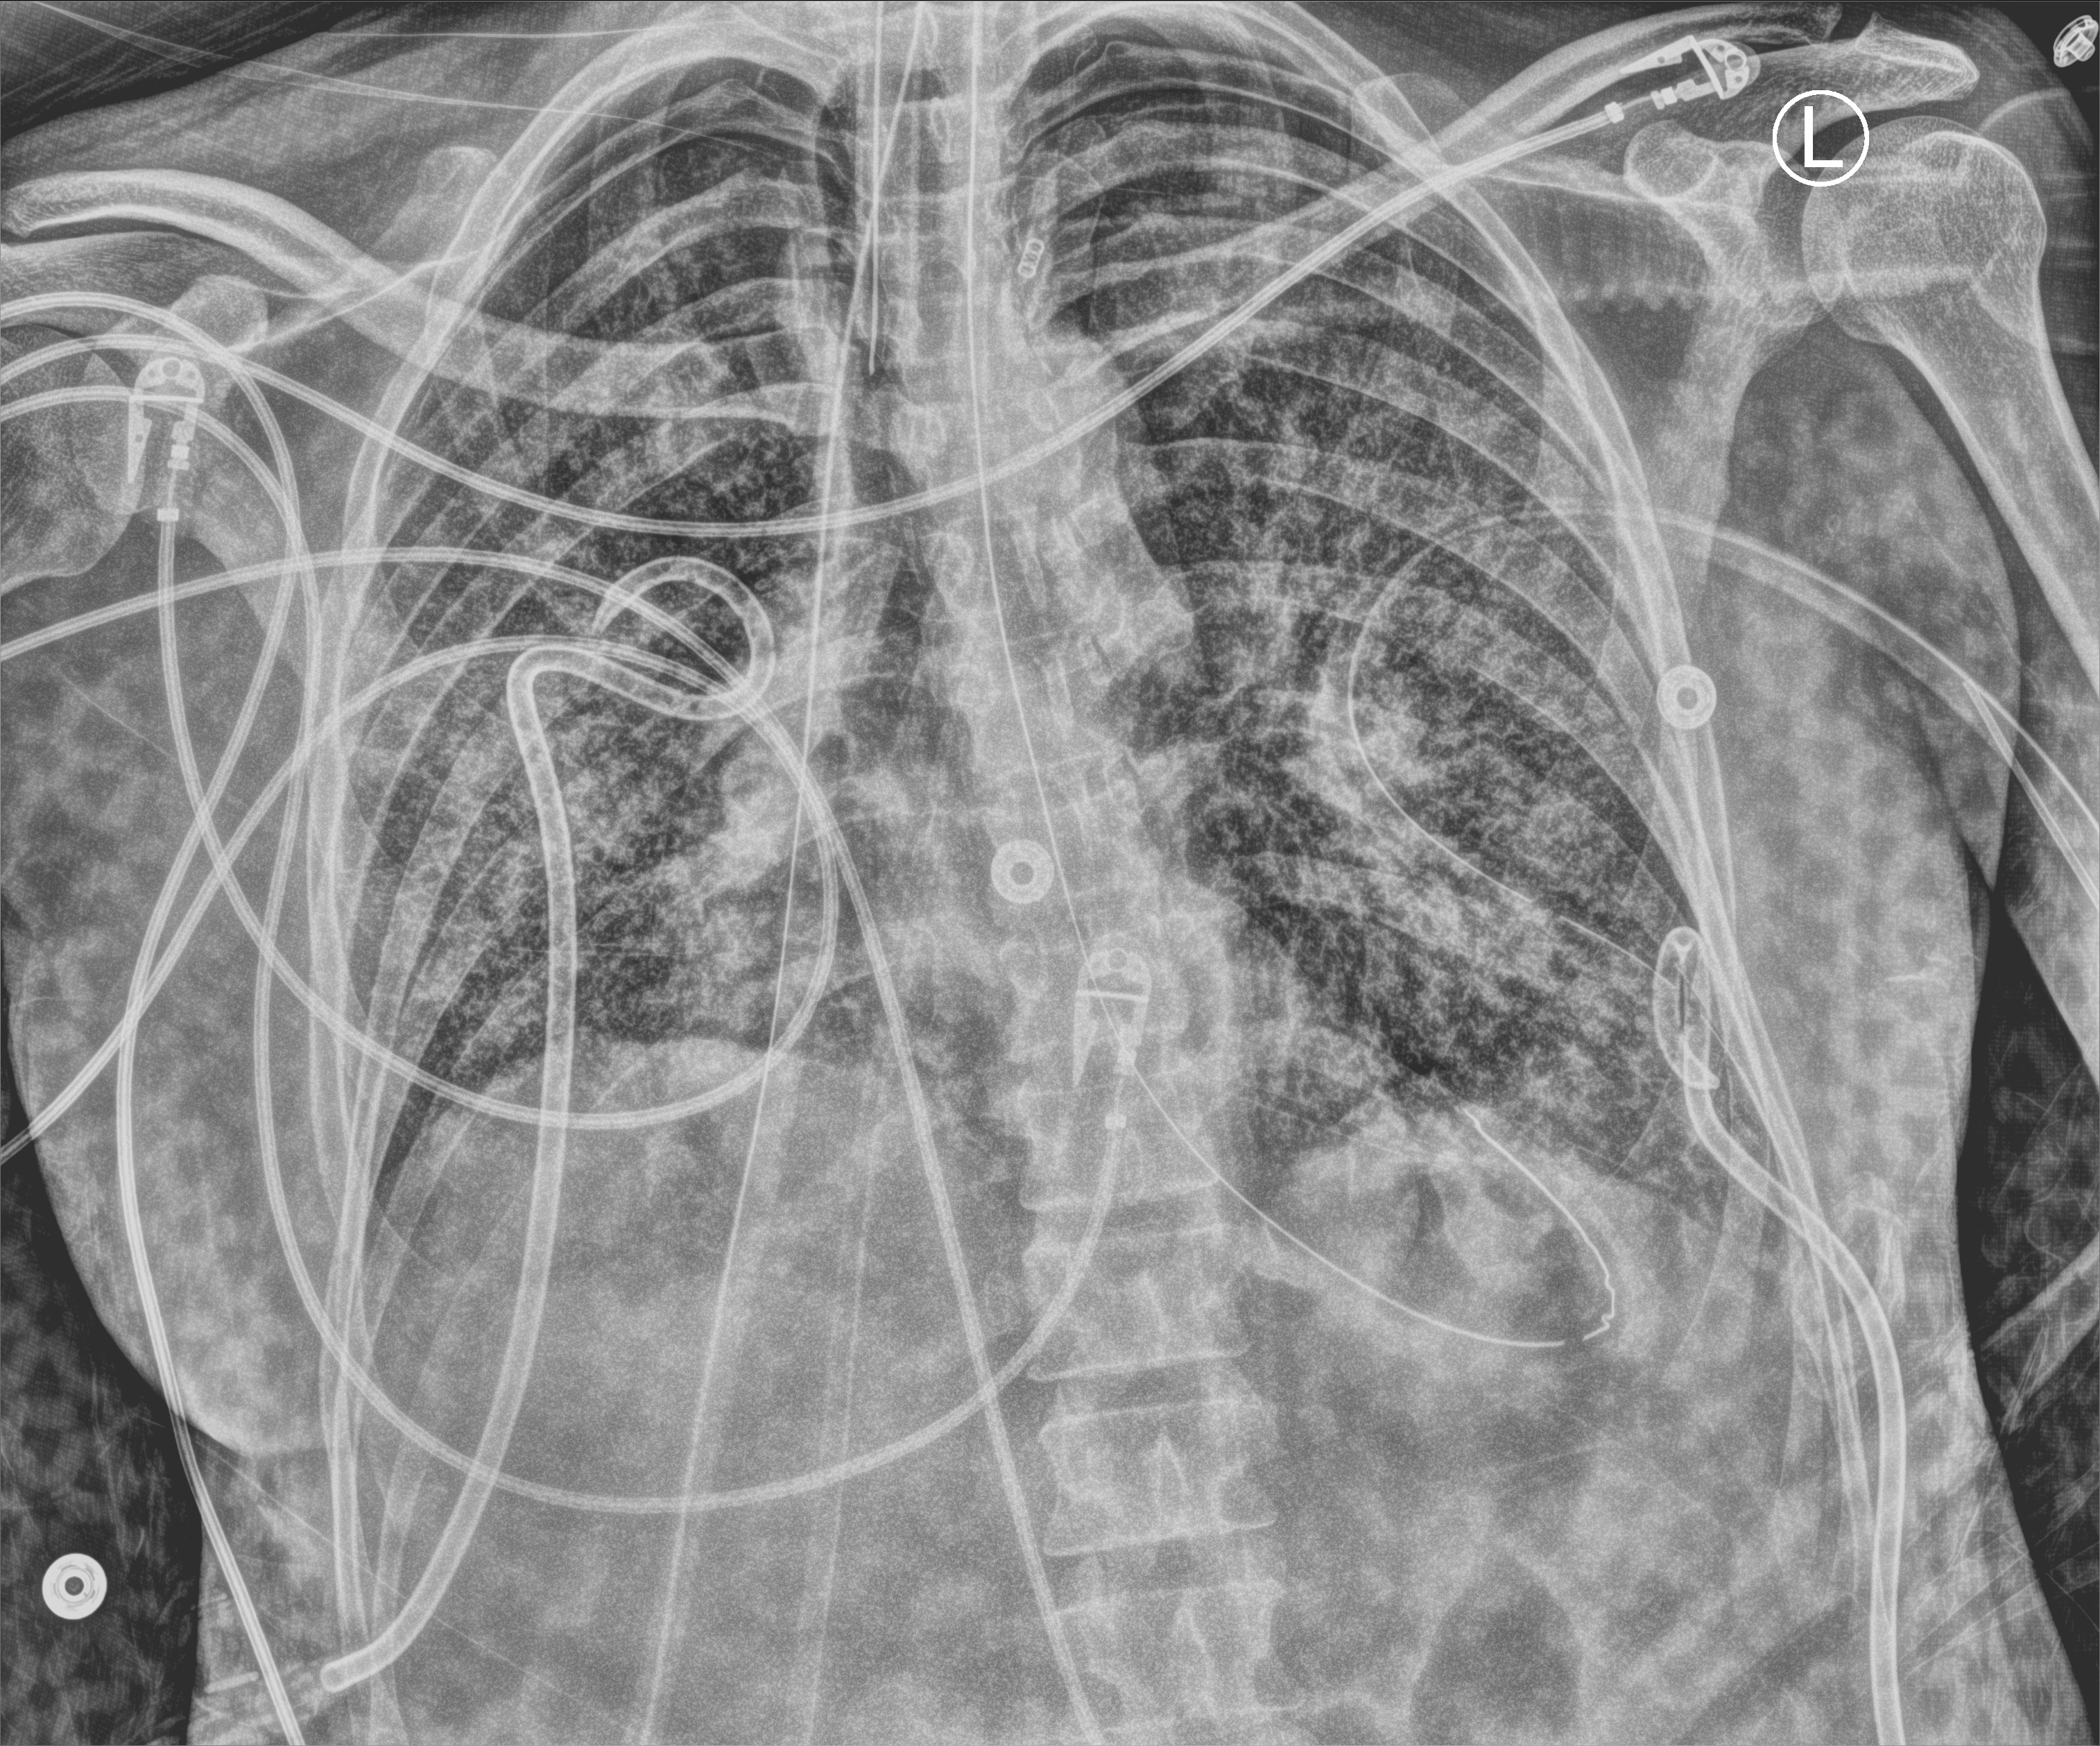
Portable chest radiograph, anteroposterior (AP) projection. Patient hospitalised with COVID-19, aged 18–59 years.
Admission-level facts for this patient (not findings on this image; timing relative to this image not recorded):
- admitted to intensive care during this hospital stay: yes